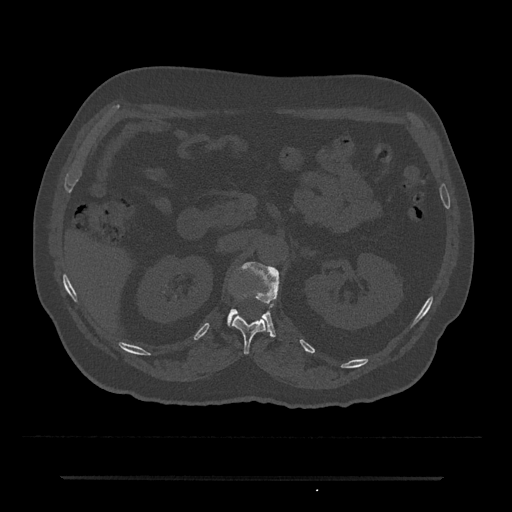
CT including the spine, one axial slice; position 104 of 797 along the scan axis; reconstruction kernel Br40s/3; 120 kVp; bone window (W 1800 / L 400 HU); 0.5 mm slice thickness; 512 × 512 image matrix. Male patient, age 69 years. Case-level facts recorded for this patient, not image findings: primary cancer: prostate.
Structures marked on this image (semi-automatically segmented with operator editing):
- L1 vertebra: box from (x=227, y=262) to (x=279, y=337) px
- T12 vertebra: (x=232, y=313)–(x=267, y=354)